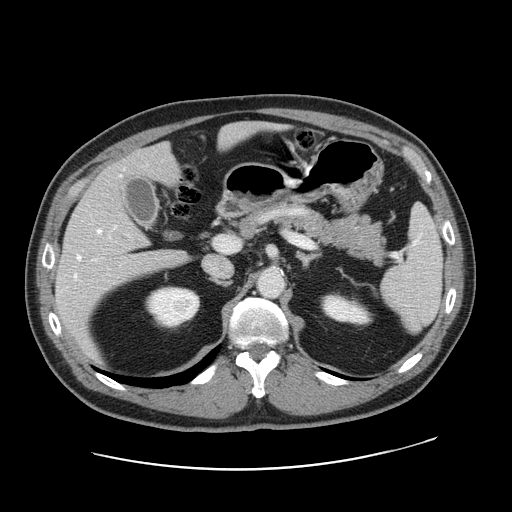
Contrast-enhanced abdominal CT, one axial slice; intravenous contrast given; soft-tissue window (W 400 / L 40 HU); 2.5 mm slice thickness; 512 × 512 image matrix, field of view 403 × 403 mm. Male patient, age 63 years. Case-level facts recorded for this patient, not image findings: diagnosis: colorectal cancer liver metastases, imaged before liver resection; multiple liver metastases: yes; largest metastasis: 8 cm; disease in both lobes: yes.
Outlined on this slice (outlined manually by an expert reader):
- hepatic veins: box from (x=75, y=175) to (x=121, y=277) px
- liver: (x=55, y=123)–(x=268, y=354)
- planned liver remnant (the part of the liver to remain after resection): (x=118, y=123)–(x=263, y=185)
- portal vein (with intrahepatic branches): (x=95, y=237)–(x=239, y=260)